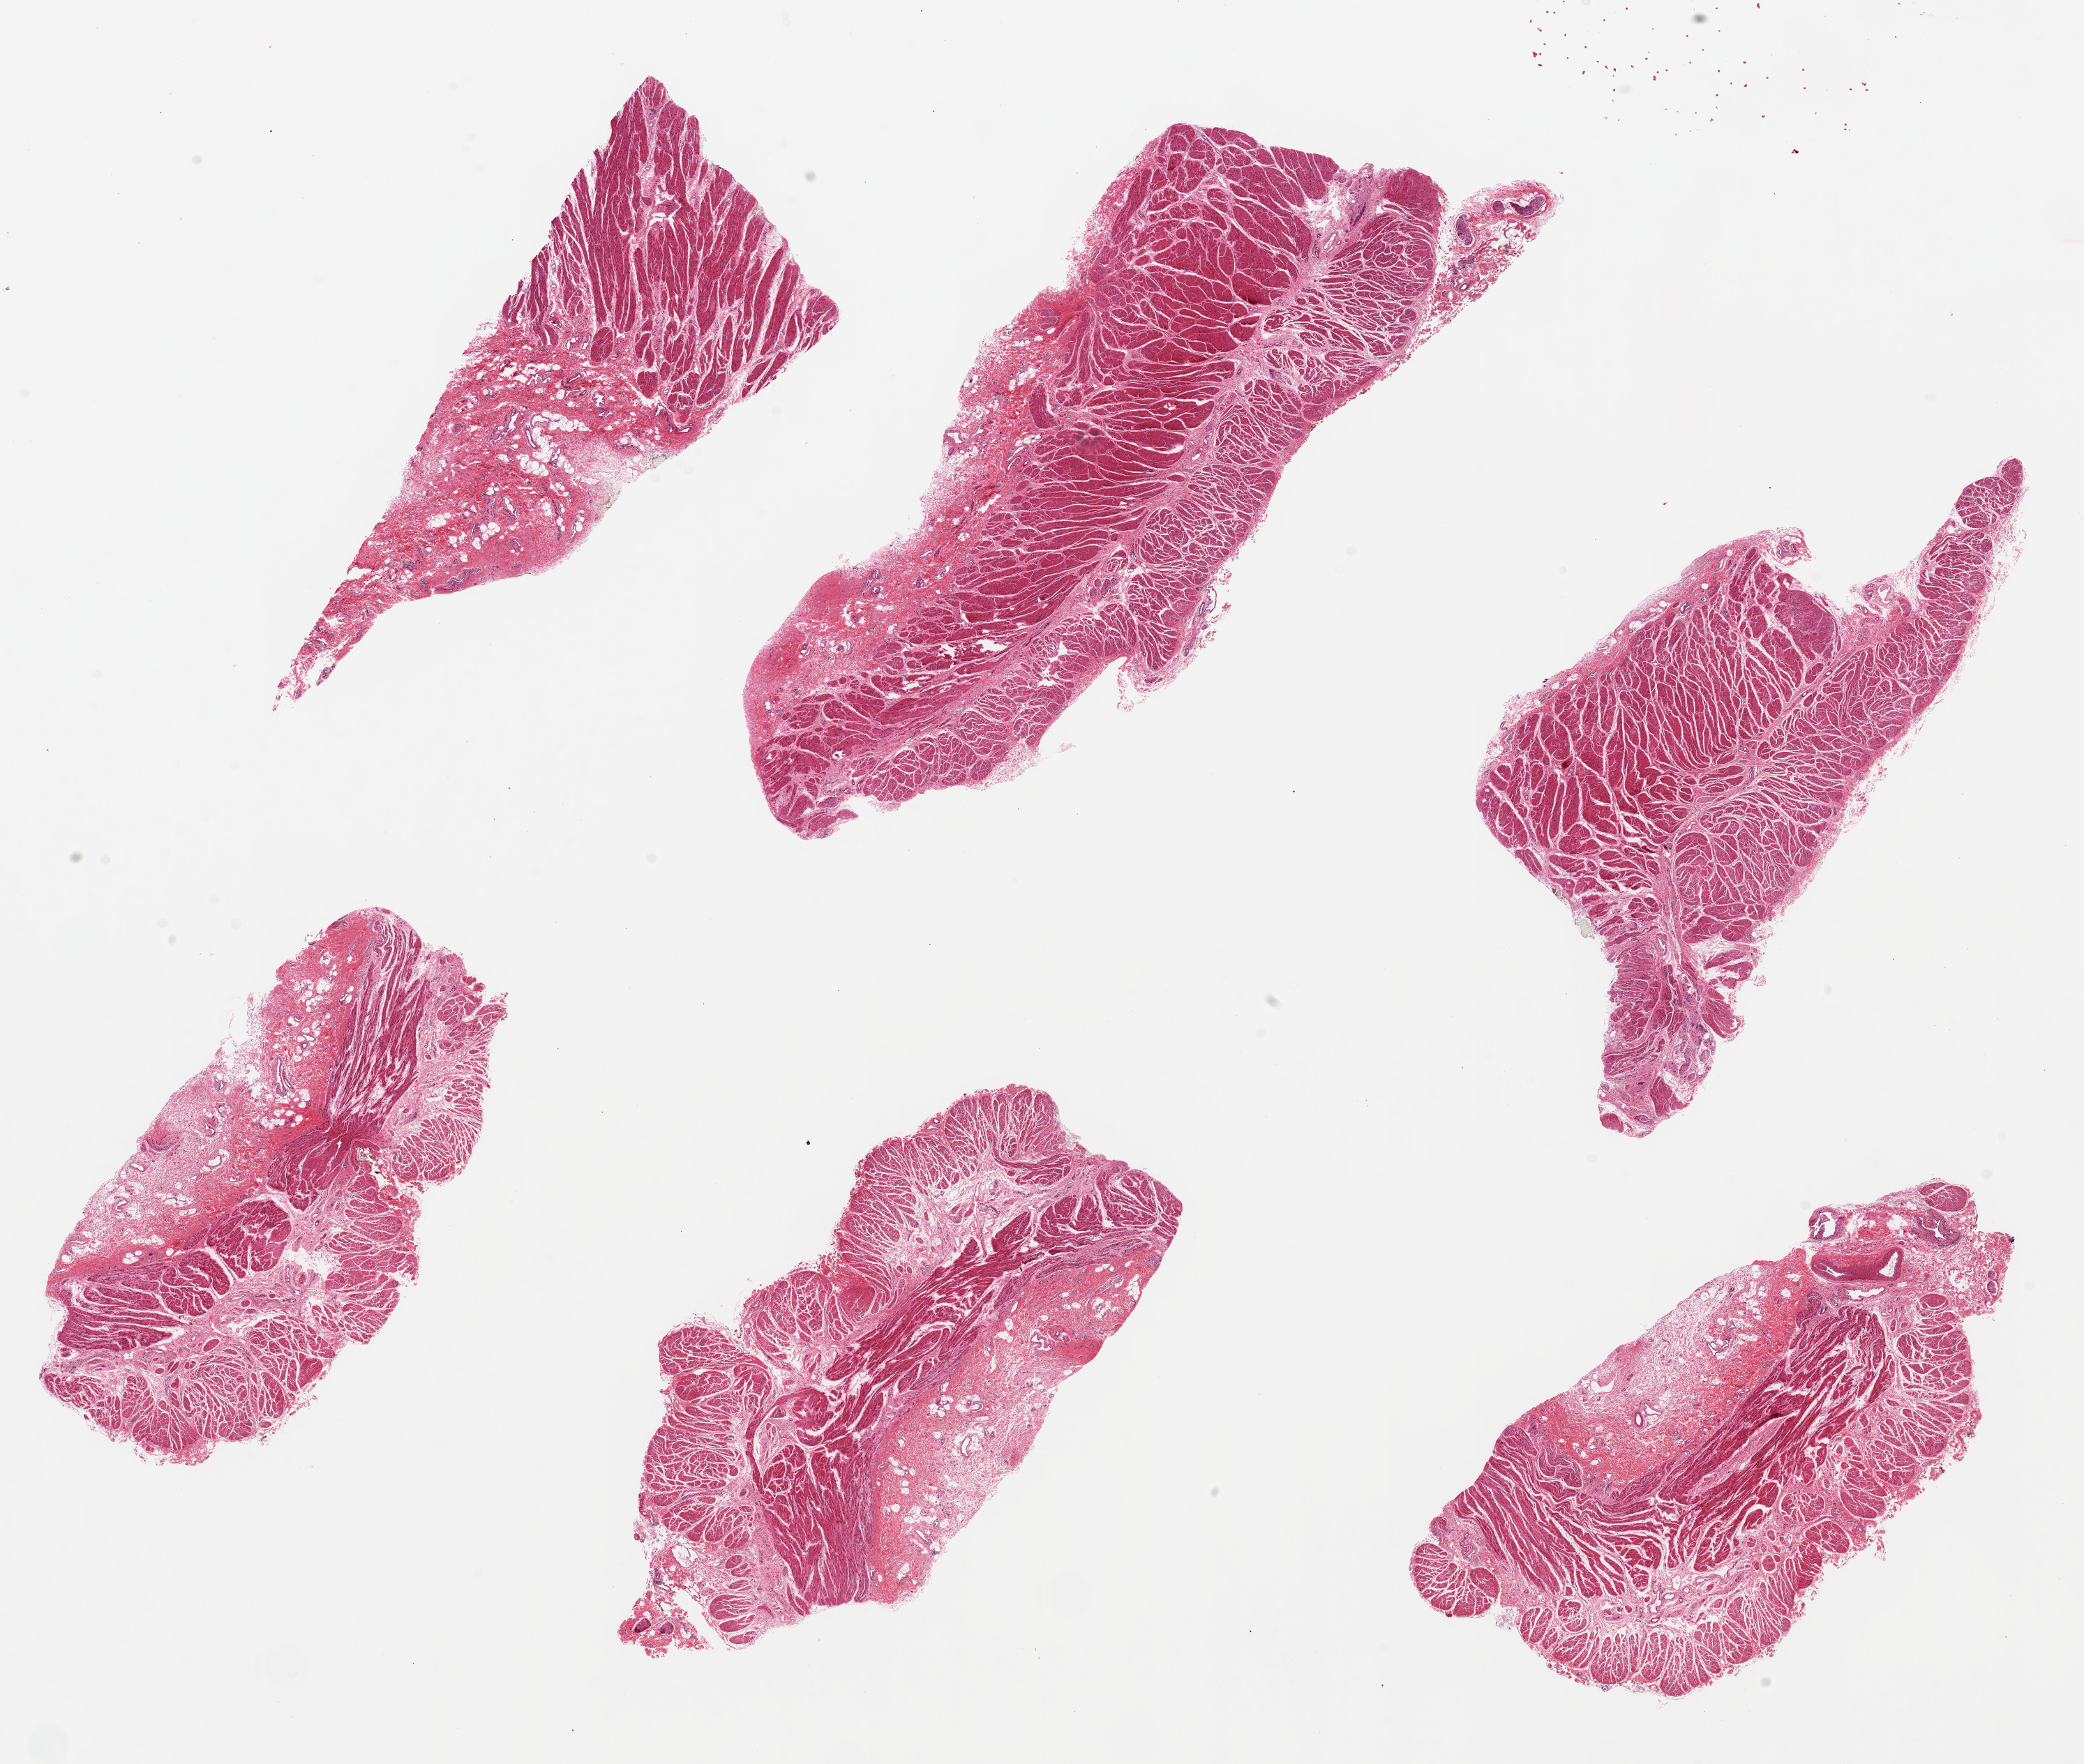
Whole-slide image, haematoxylin and eosin stain, low-resolution overview of the scanned area, about 23.6 x 20.0 mm (acquisition: 20x scan). PAXgene-fixed paraffin-embedded (PFPE) section. Sampled site (target tissue): gastroesophageal junction. Tissue donor sample.
- review note (as recorded): 6 pieces ~8x4mm. All muscle, no mucosa, excellent specimens